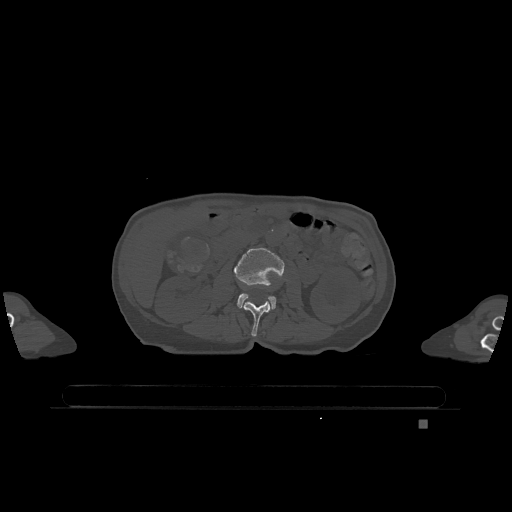
CT including the spine, one axial slice; position 390 of 1317 along the scan axis; bone window (W 1800 / L 400 HU); 0.5 mm slice thickness; 512 × 512 image matrix. Female patient, age 74 years. Case-level facts recorded for this patient, not image findings: primary cancer: lung.
Outlined on this slice (semi-automatically segmented with operator editing):
- L2 vertebra: bounding box [x1, y1, x2, y2] px = [243, 301, 270, 337]
- L3 vertebra: [234, 248, 284, 309]